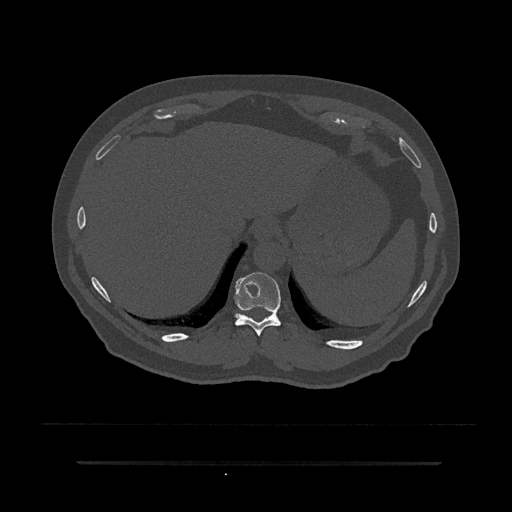
CT including the spine, one axial slice. Slice 321 of 797 in the series (ordered by position). Reconstruction kernel Br40s/3. 120 kVp. Bone window (W 1800 / L 400 HU). 0.5 mm slice thickness. 512 × 512 image matrix, field of view 464 × 464 mm. Patient: male, 59 years. Case-level facts recorded for this patient, not image findings: primary cancer: bile ducts; vertebrae with lytic lesions (as recorded): T10.
Structures marked on this image (semi-automatically segmented with operator editing):
- T10 vertebra: bounding box [x1, y1, x2, y2] px = [233, 272, 281, 336]